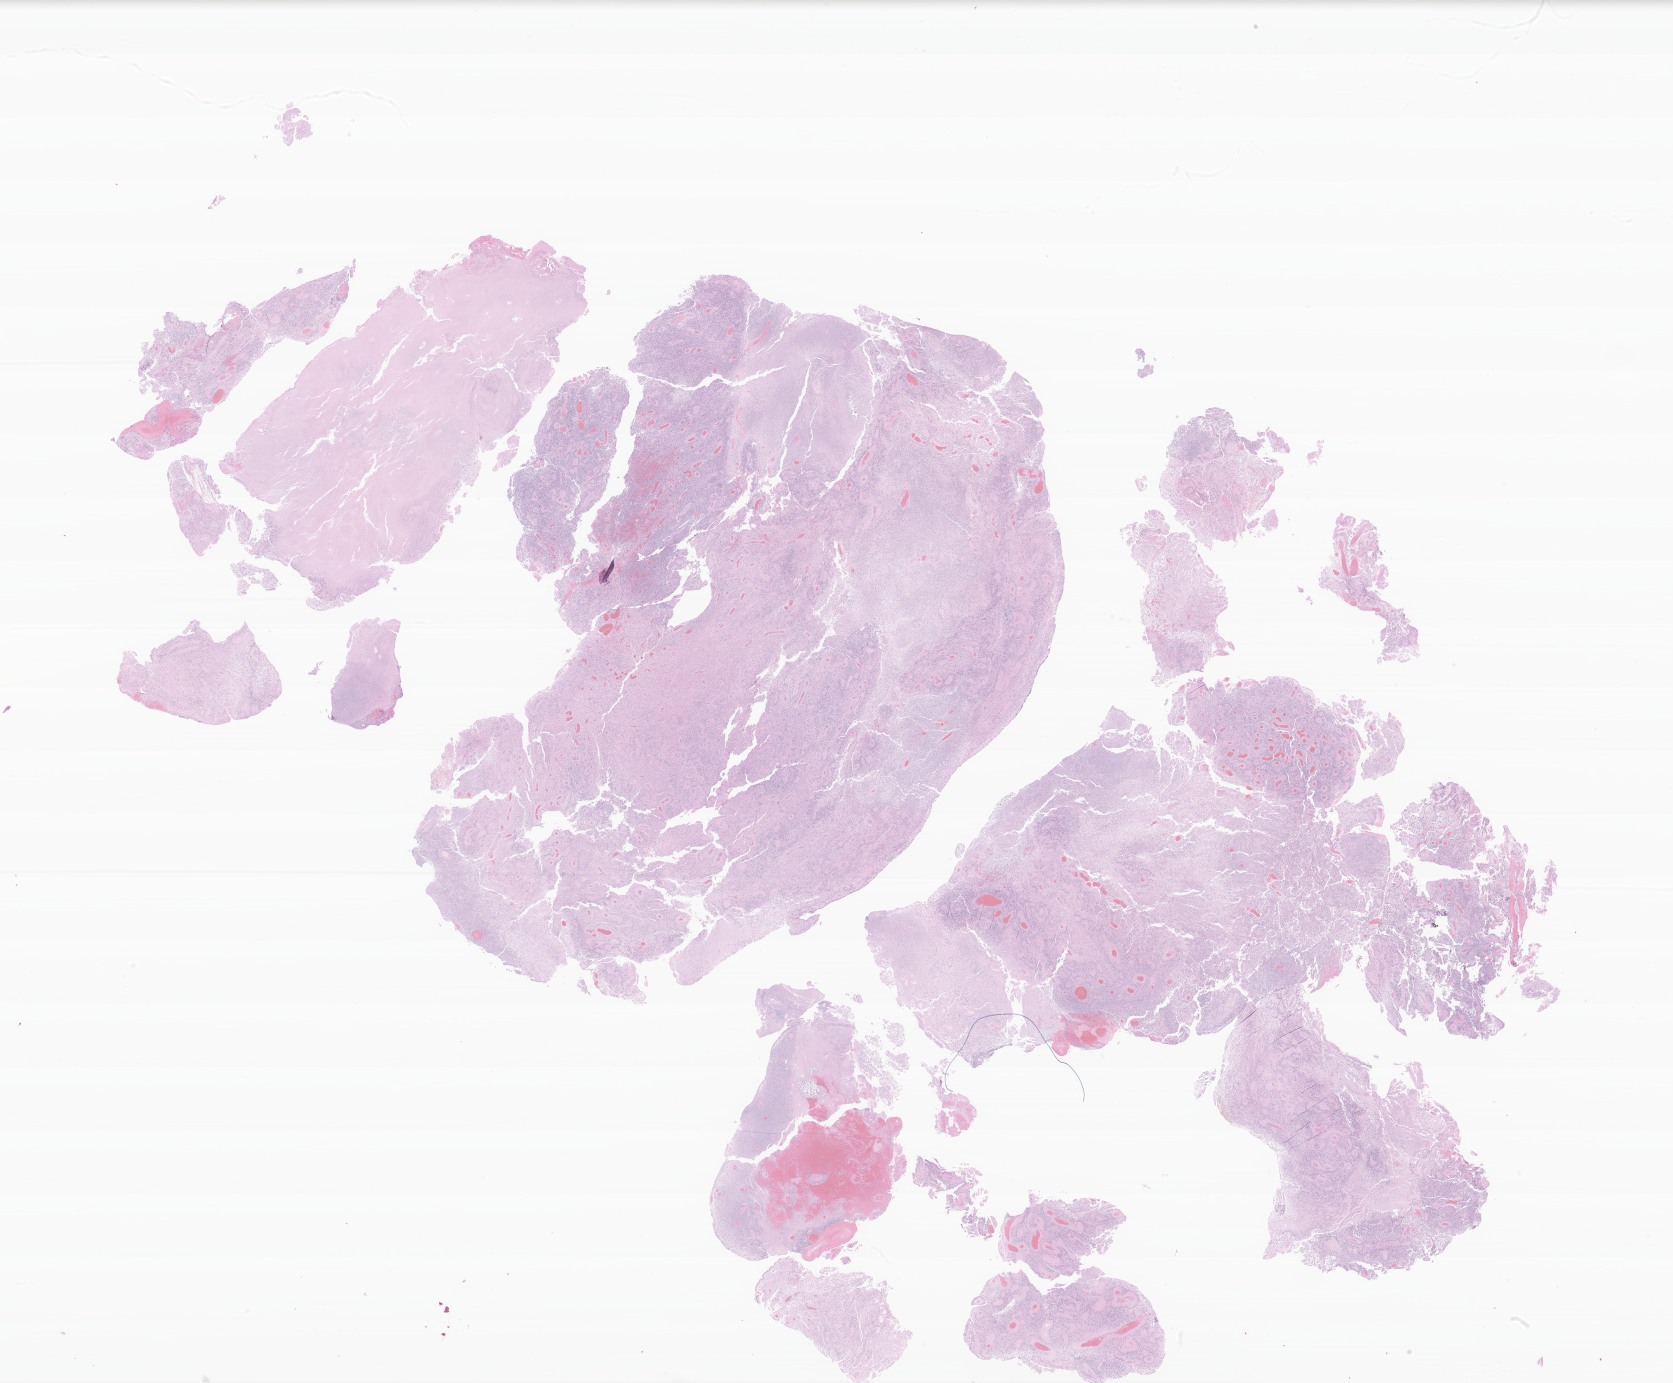
Whole-slide image, hematoxylin and eosin (H&E) stain of tumor tissue from the brain, a low-resolution overview of the entire scanned area, about 28.1 x 23.3 mm; formalin-fixed, paraffin-embedded (FFPE) tissue. Patient male; age 356 days.
• diagnosis (ICD-O-3 morphology term): Ependymoma, NOS